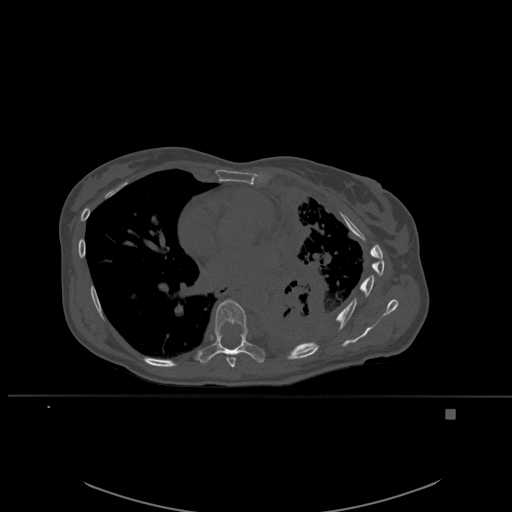
CT including the spine, one axial slice. Slice 354 of 537 in the series (ordered by position). Bone window (W 1800 / L 400 HU). 1.5 mm slice thickness. 512 × 512 image matrix. Patient: female, 45 years. Case-level facts recorded for this patient, not image findings: primary cancer: lung.
Outlined on this slice (semi-automatic segmentation, software-assisted and operator-edited):
- T7 vertebra: bounding box (x1, y1, x2, y2) in pixels: (226, 357, 236, 368)
- T8 vertebra: (196, 299, 265, 364)